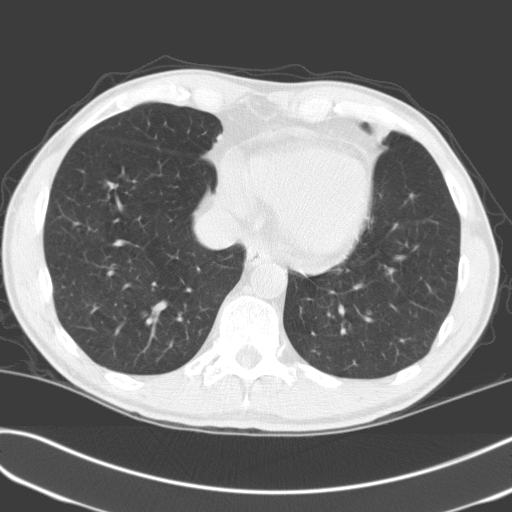
Low-dose screening chest CT, one axial slice; slice 51 of 170 in the series (ordered by position); 120 kVp; lung window (W 1500 / L -600 HU); 3.2 mm slice thickness; 512 × 512 image matrix, field of view 351 × 351 mm.
Outlined on this slice (manually delineated by an expert):
- lesion 1 (tumor, upper lobe of left lung): bounding box <367,121,392,143> (left, top, right, bottom; pixels)